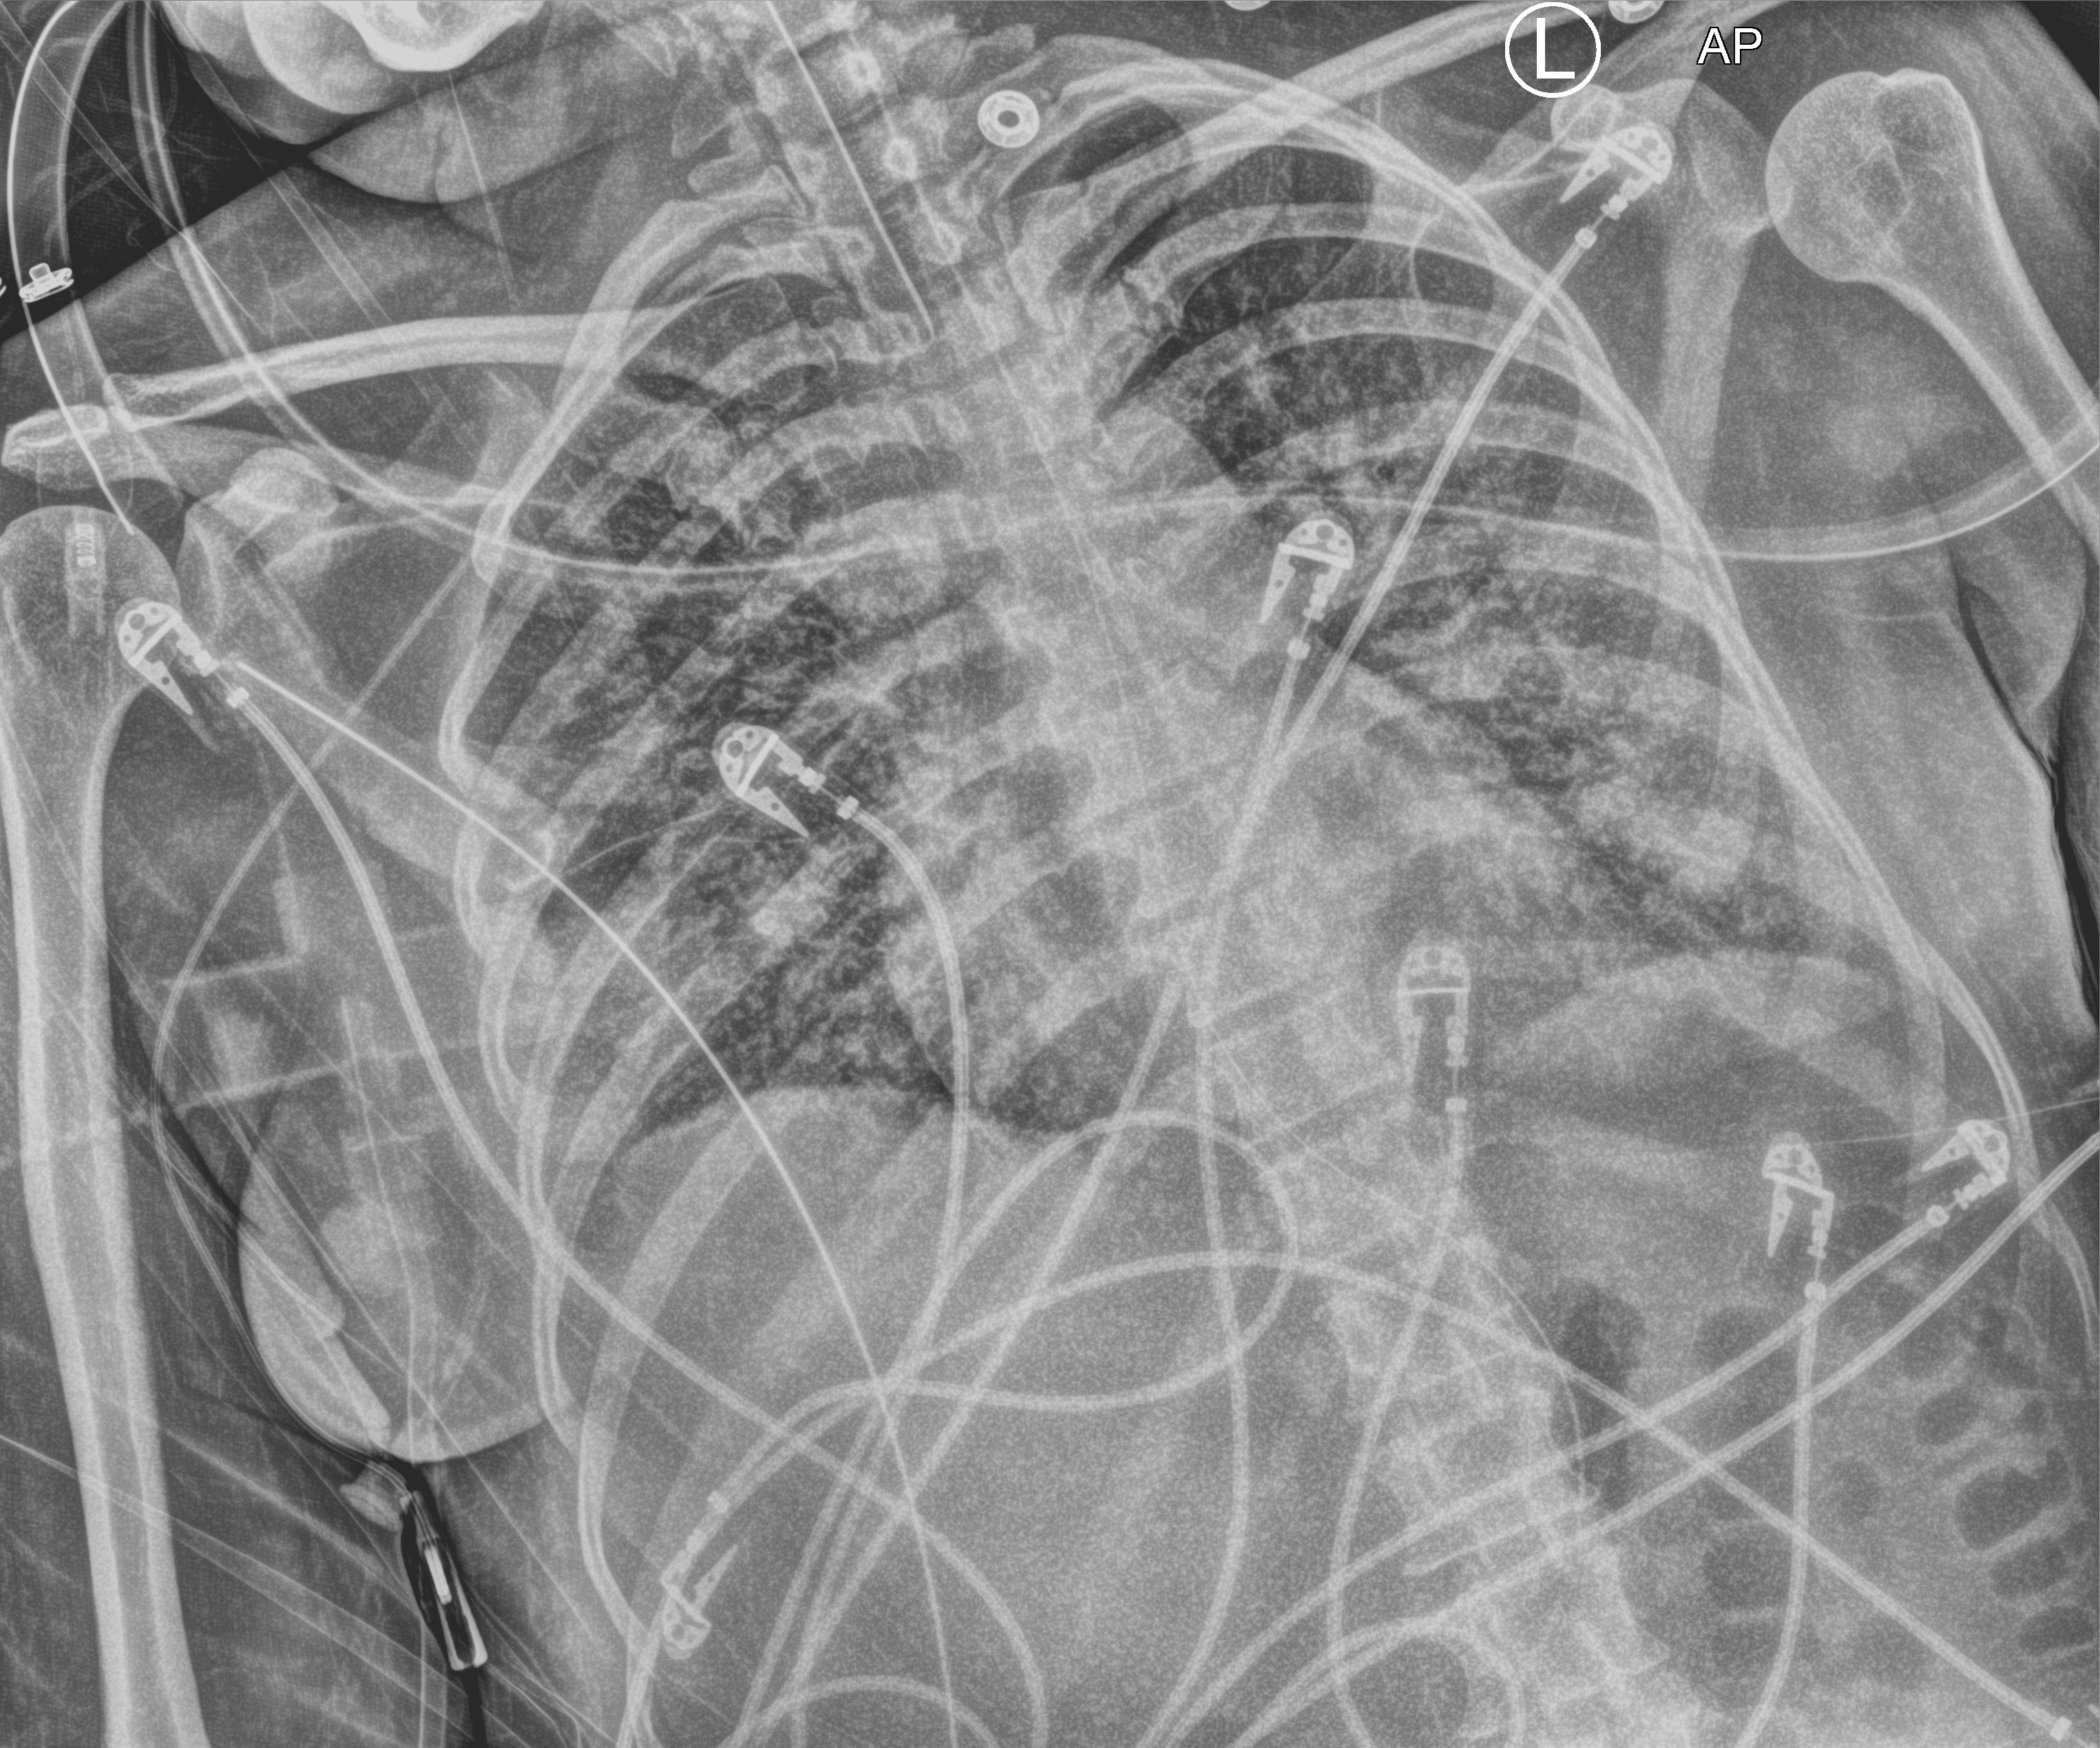
Chest X-ray (portable), anteroposterior (AP) projection. Female patient hospitalised with COVID-19, age 18–59 years.
From the hospital-stay record, not from the radiograph (when in the stay this image was taken is not recorded): COPD (admission record): no; length of hospital stay: 71 days; chronic kidney disease (admission record): no.